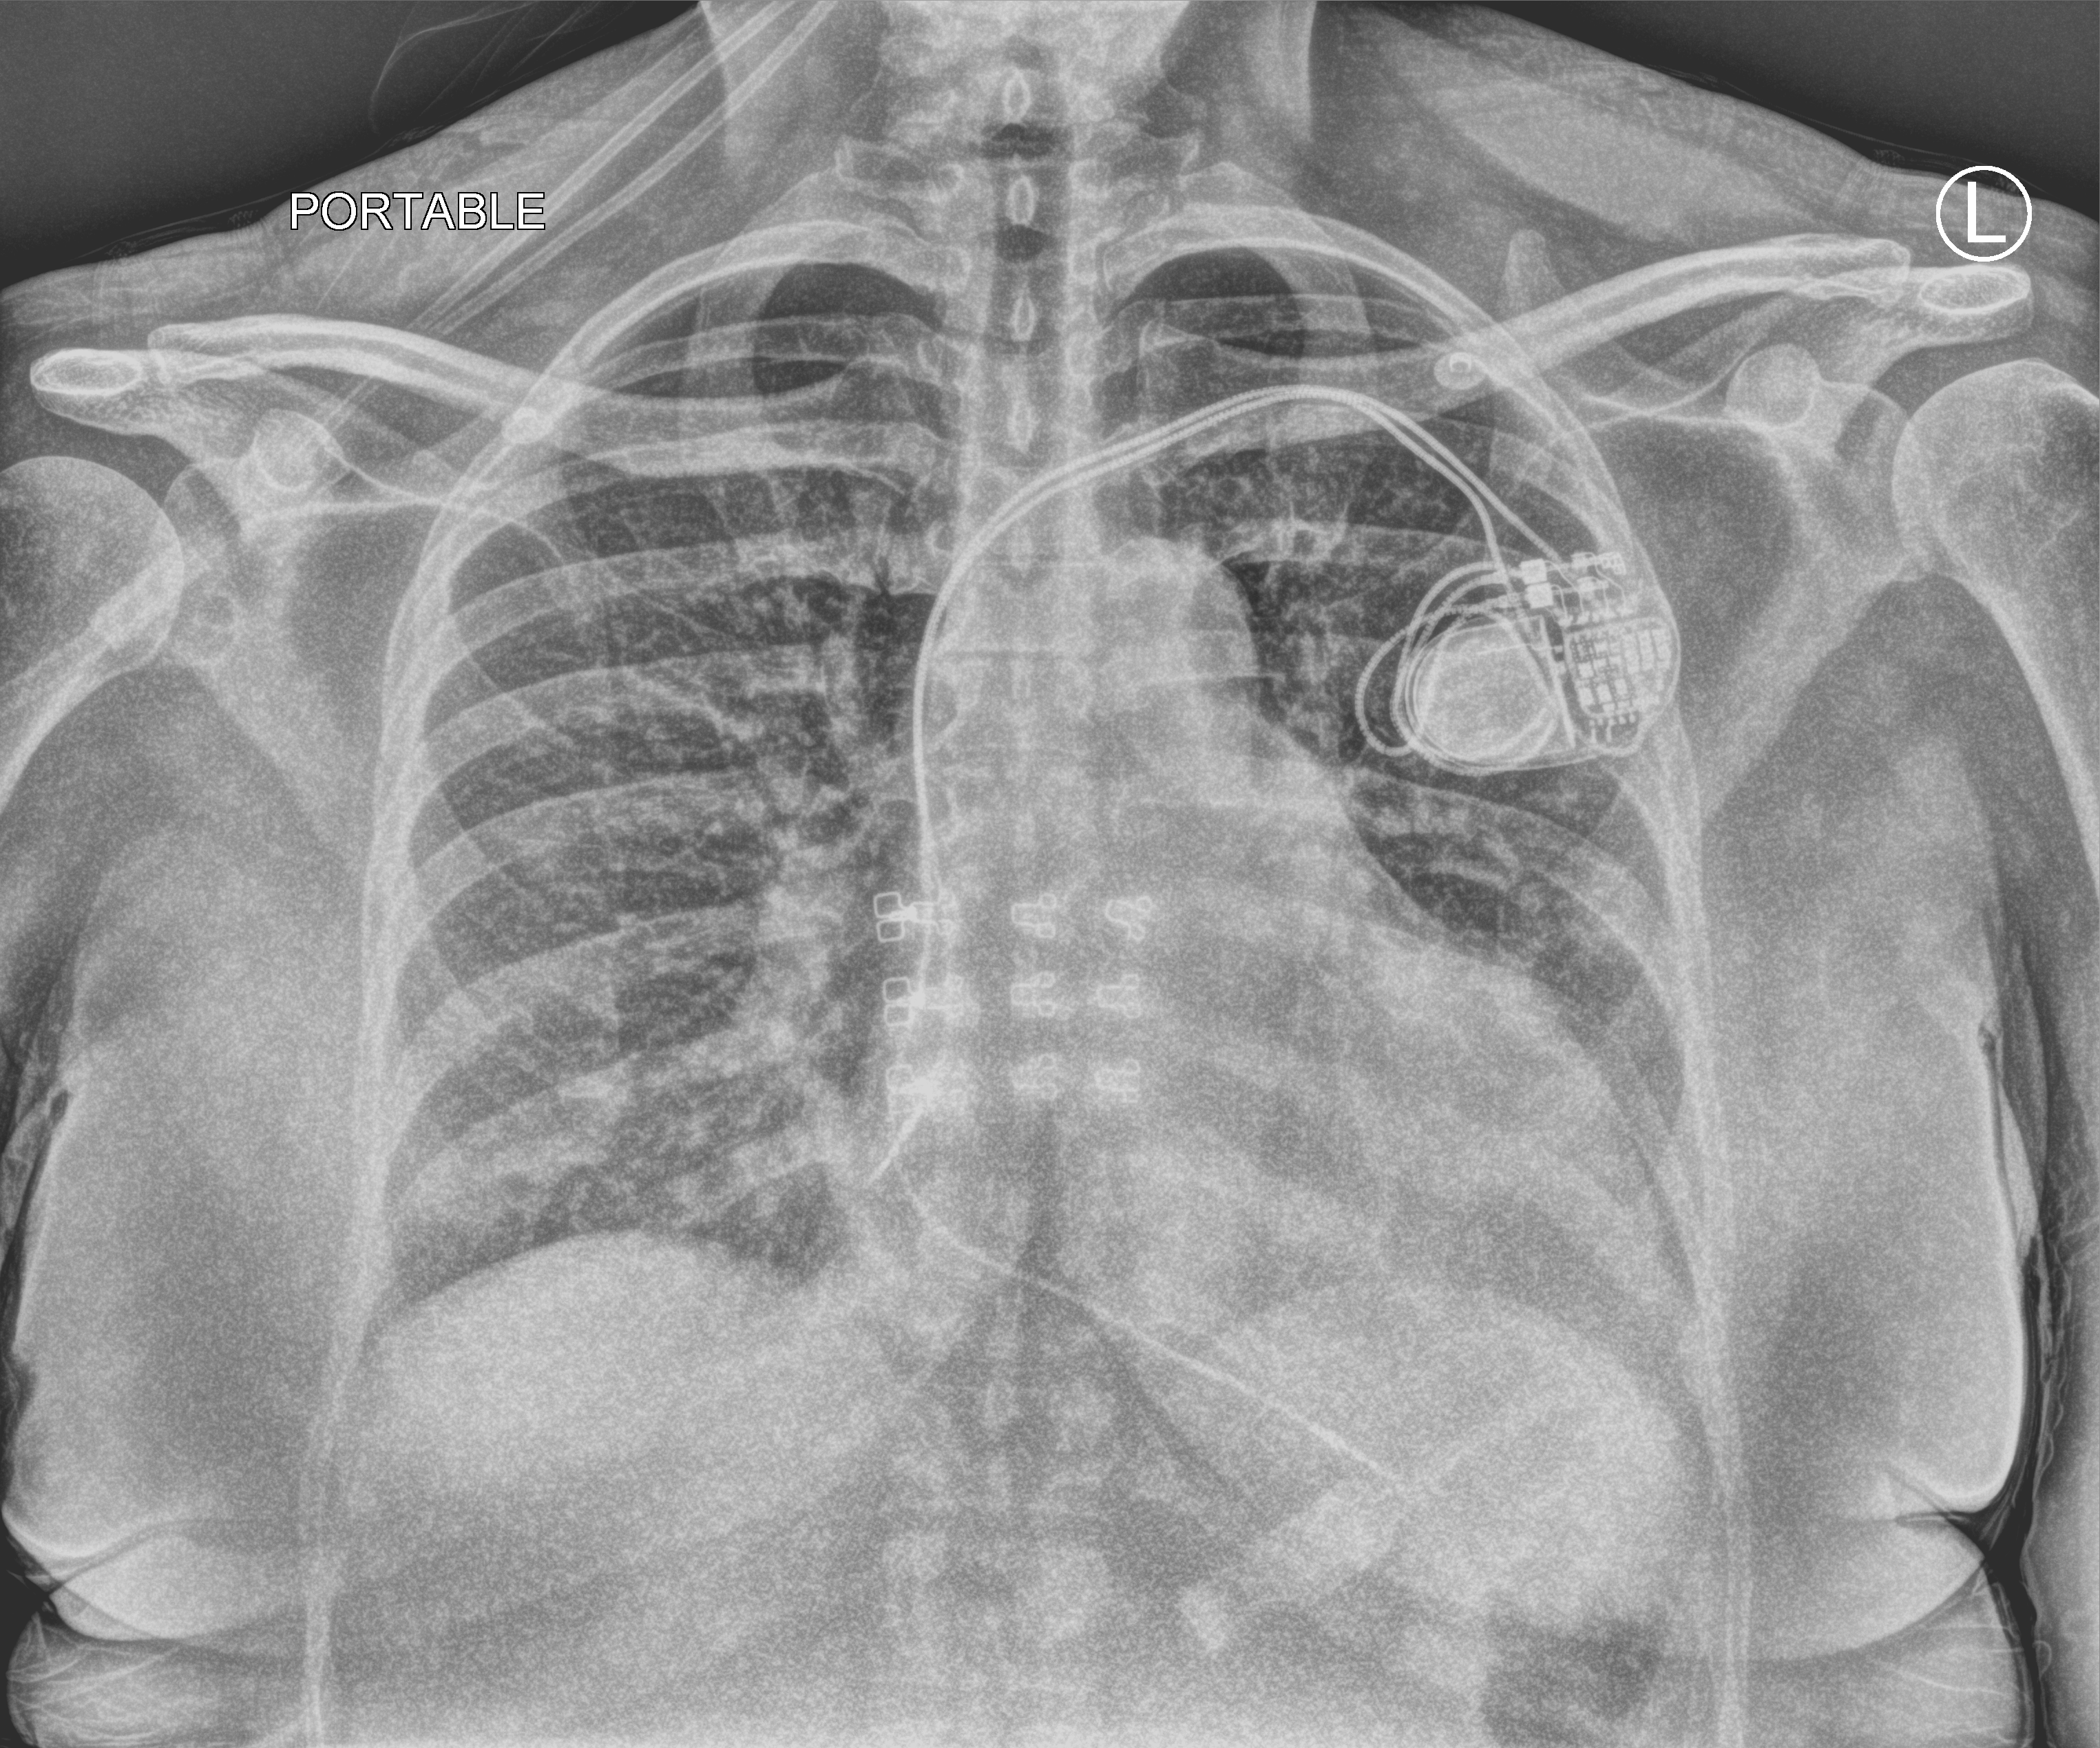
Portable chest radiograph, anteroposterior (AP) projection. Patient hospitalised with COVID-19; female, aged 18–59 years.
From the hospital-stay record, not from the radiograph (when in the stay this image was taken is not recorded):
- admitted to intensive care during this hospital stay: no
- mechanically ventilated during this hospital stay: no